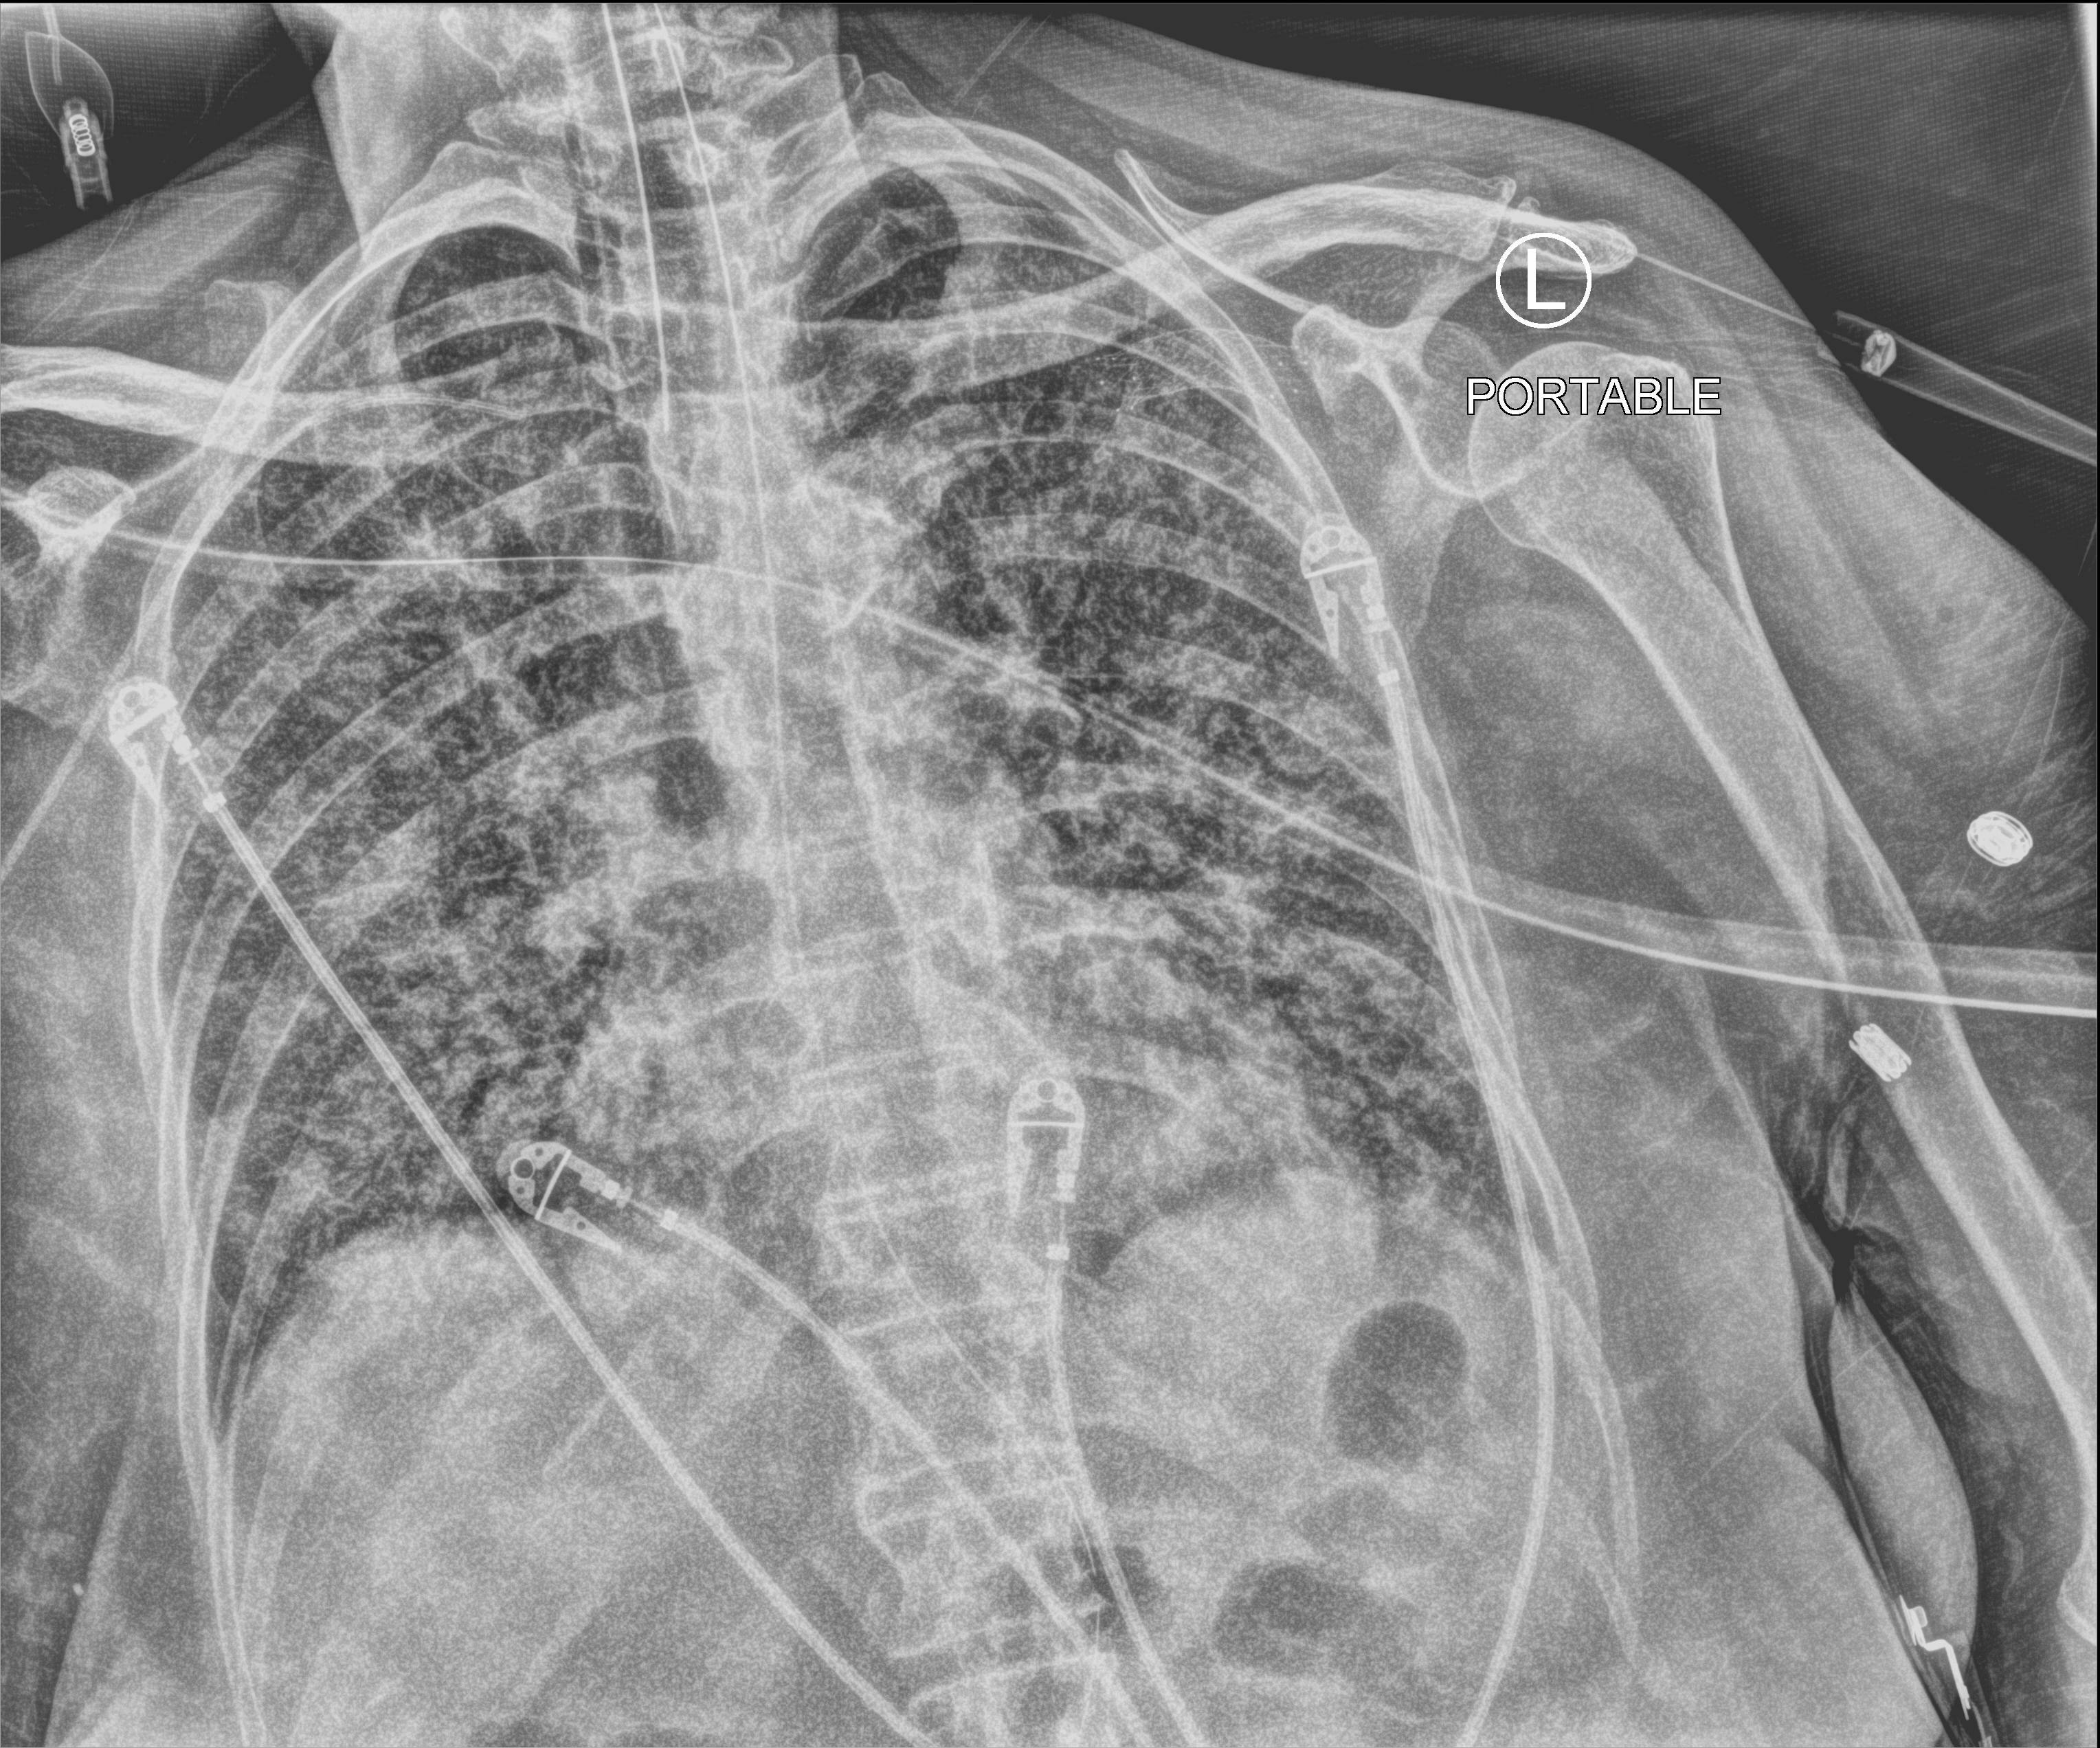
Bedside chest radiograph (computed radiography), anteroposterior (AP) projection. Female patient hospitalised with COVID-19, age 60–74 years.
Hospital-stay facts (about this admission, not read from this image; timing relative to this image not recorded): length of hospital stay: 23 days; COPD (admission record): no; mechanically ventilated during this hospital stay: yes.